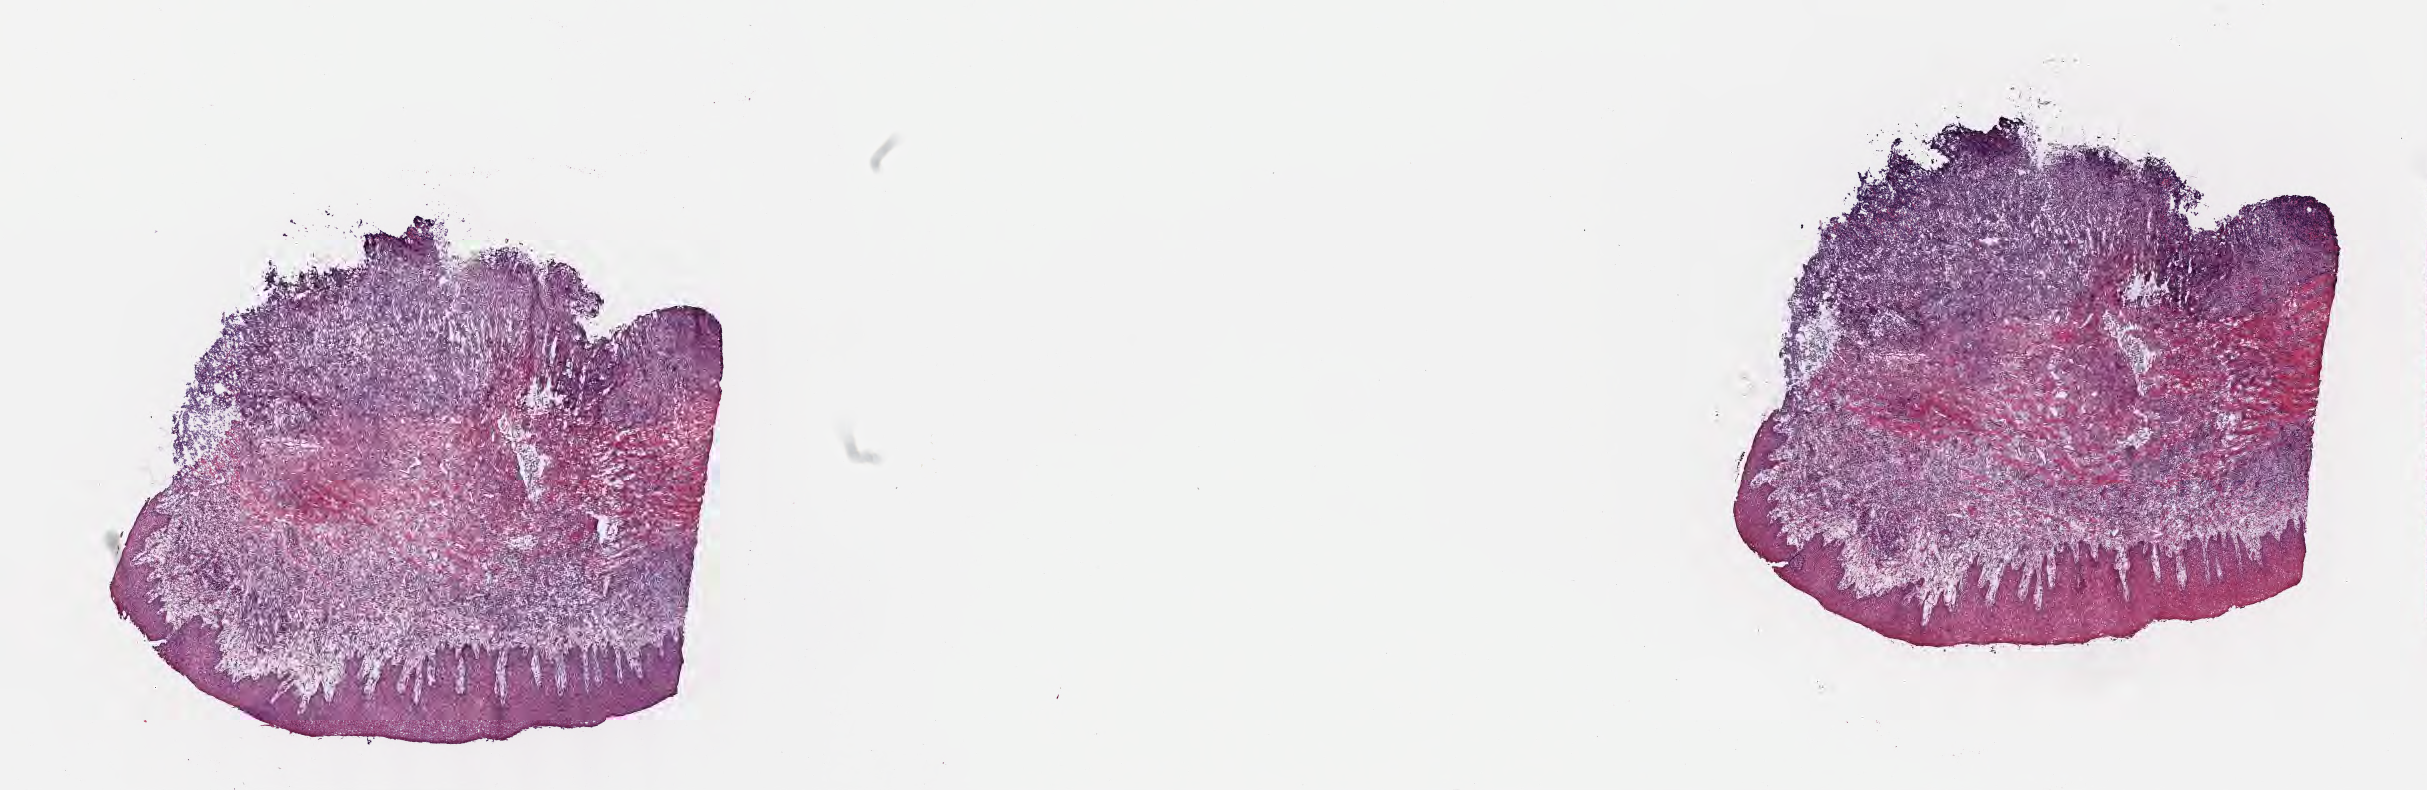
Digitized hematoxylin and eosin (H&E)-stained section, whole scanned area (about 19.6 x 6.4 mm) shown as a low-resolution overview. Cryosection. Primary tumor. Site: cranium. Patient male; 10 years old. Composition of this section per pathologist review: tumor cells 30%, tumor nuclei 40%.
Diagnosis: Burkitt lymphoma, NOS.